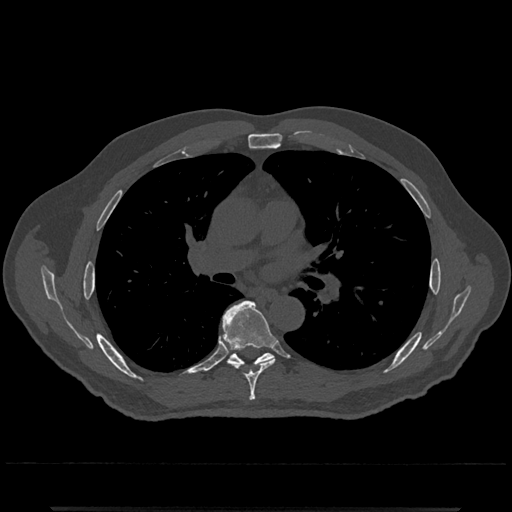
CT including the spine, one axial slice; slice 753 of 797 in the series (ordered by position); reconstruction kernel Br40s/3; 120 kVp; bone window (W 1800 / L 400 HU); 512 × 512 image matrix, field of view 393 × 393 mm. Patient: male, 67 years. From the clinical record (not read from this slice): primary cancer: prostate.
Outlined on this slice (semi-automatically segmented with operator editing):
- T6 vertebra: bounding box <221,300,275,401> (left, top, right, bottom; pixels)
- T7 vertebra: <228,348,274,367>